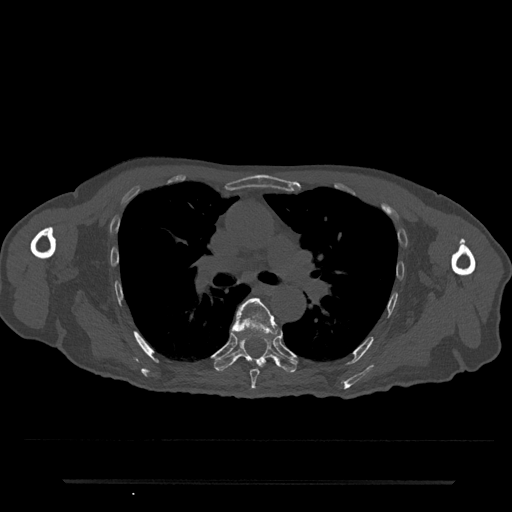
CT including the spine, one axial slice; slice 505 of 797 in the series (ordered by position); reconstruction kernel Br40s/3; bone window (W 1800 / L 400 HU); 0.5 mm slice thickness; 512 × 512 image matrix. Patient: male, 74 years. Case-level facts recorded for this patient, not image findings: primary cancer: prostate.
Annotated regions visible in this slice (semi-automatically segmented with operator editing):
- T6 vertebra: box from (x=231, y=298) to (x=279, y=390) px
- T7 vertebra: (x=215, y=339)–(x=297, y=372)